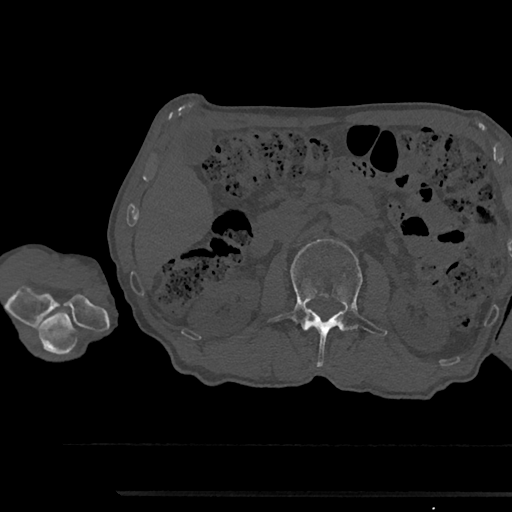
CT including the spine, one axial slice; 120 kVp; bone window (W 1800 / L 400 HU); 0.5 mm slice thickness; 512 × 512 image matrix. Male patient, age 79 years. Case-level facts recorded for this patient, not image findings: primary cancer: prostate.
Annotated regions visible in this slice (semi-automatically segmented with operator editing):
- L2 vertebra: box from (x=268, y=239) to (x=387, y=367) px